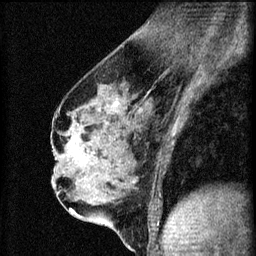
Breast MRI (dynamic contrast-enhanced), one sagittal slice; slice 35 of 60 in the series (ordered by position); 3 images stored at this slice position (order not interpretable as contrast timing); 1.5 T; TE 4.2 ms, TR 8.2 ms; 2 mm slice thickness; 256 × 256 image matrix, field of view 180 × 180 mm. Patient: female, 56 years.
Outlined on this slice (semi-automatically segmented with operator editing):
- analysis volume of interest (the breast-tissue region the enhancement analysis was run in; not a lesion): bounding box <62,136,111,179> (left, top, right, bottom; pixels)
- tumour enhancement mask (voxels above the 70 % enhancement threshold inside the analysis volume of interest): <71,136,79,159>